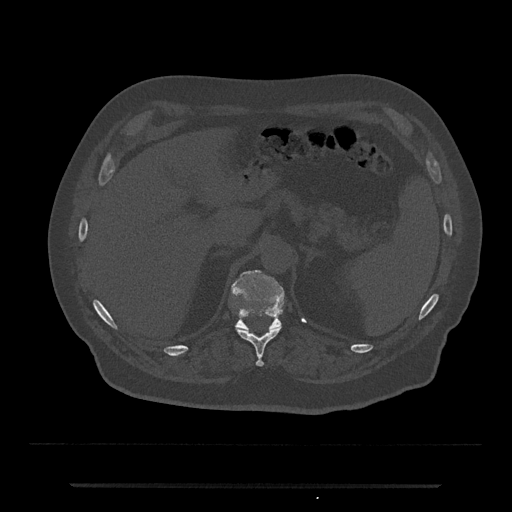
CT including the spine, one axial slice. Reconstruction kernel Br40s/3. 120 kVp. Bone window (W 1800 / L 400 HU). 0.5 mm slice thickness. 512 × 512 image matrix, field of view 434 × 434 mm. Male patient, age 80 years. Case-level facts recorded for this patient, not image findings: primary cancer: prostate; vertebrae with lytic lesions (as recorded): L1, T11.
Annotated regions visible in this slice (semi-automatically segmented with operator editing):
- T11 vertebra: bounding box [x1, y1, x2, y2] px = [237, 327, 281, 367]
- T12 vertebra: [231, 269, 285, 331]